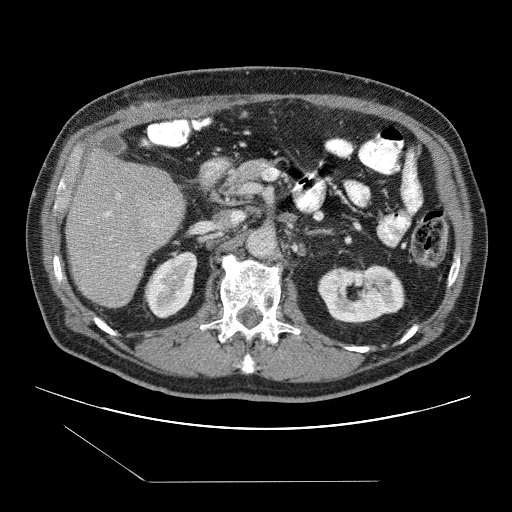
Contrast-enhanced abdominal CT (liver protocol), one axial slice; slice 40 of 109 in the series (ordered by position); reconstruction kernel STANDARD; 120 kVp; one of 2 acquisitions stored at this slice position; soft-tissue window (W 400 / L 40 HU); 2.5 mm slice thickness; 512 × 512 image matrix, field of view 400 × 400 mm. Case-level facts recorded for this patient, not image findings: diagnosis: hepatocellular carcinoma (patient treated with transarterial chemoembolisation; whether this scan precedes or follows treatment is not stated here); TNM stage (as recorded): Stage-IIIB; Child-Pugh class: A.
Annotated regions visible in this slice (semi-automatically segmented with operator editing):
- liver parenchyma outside the tumour (the mass and vessels are separate outlines, so this box may not span the whole liver): bounding box (x1, y1, x2, y2) in pixels: (66, 148, 186, 308)
- liver vessels: (105, 194, 157, 268)